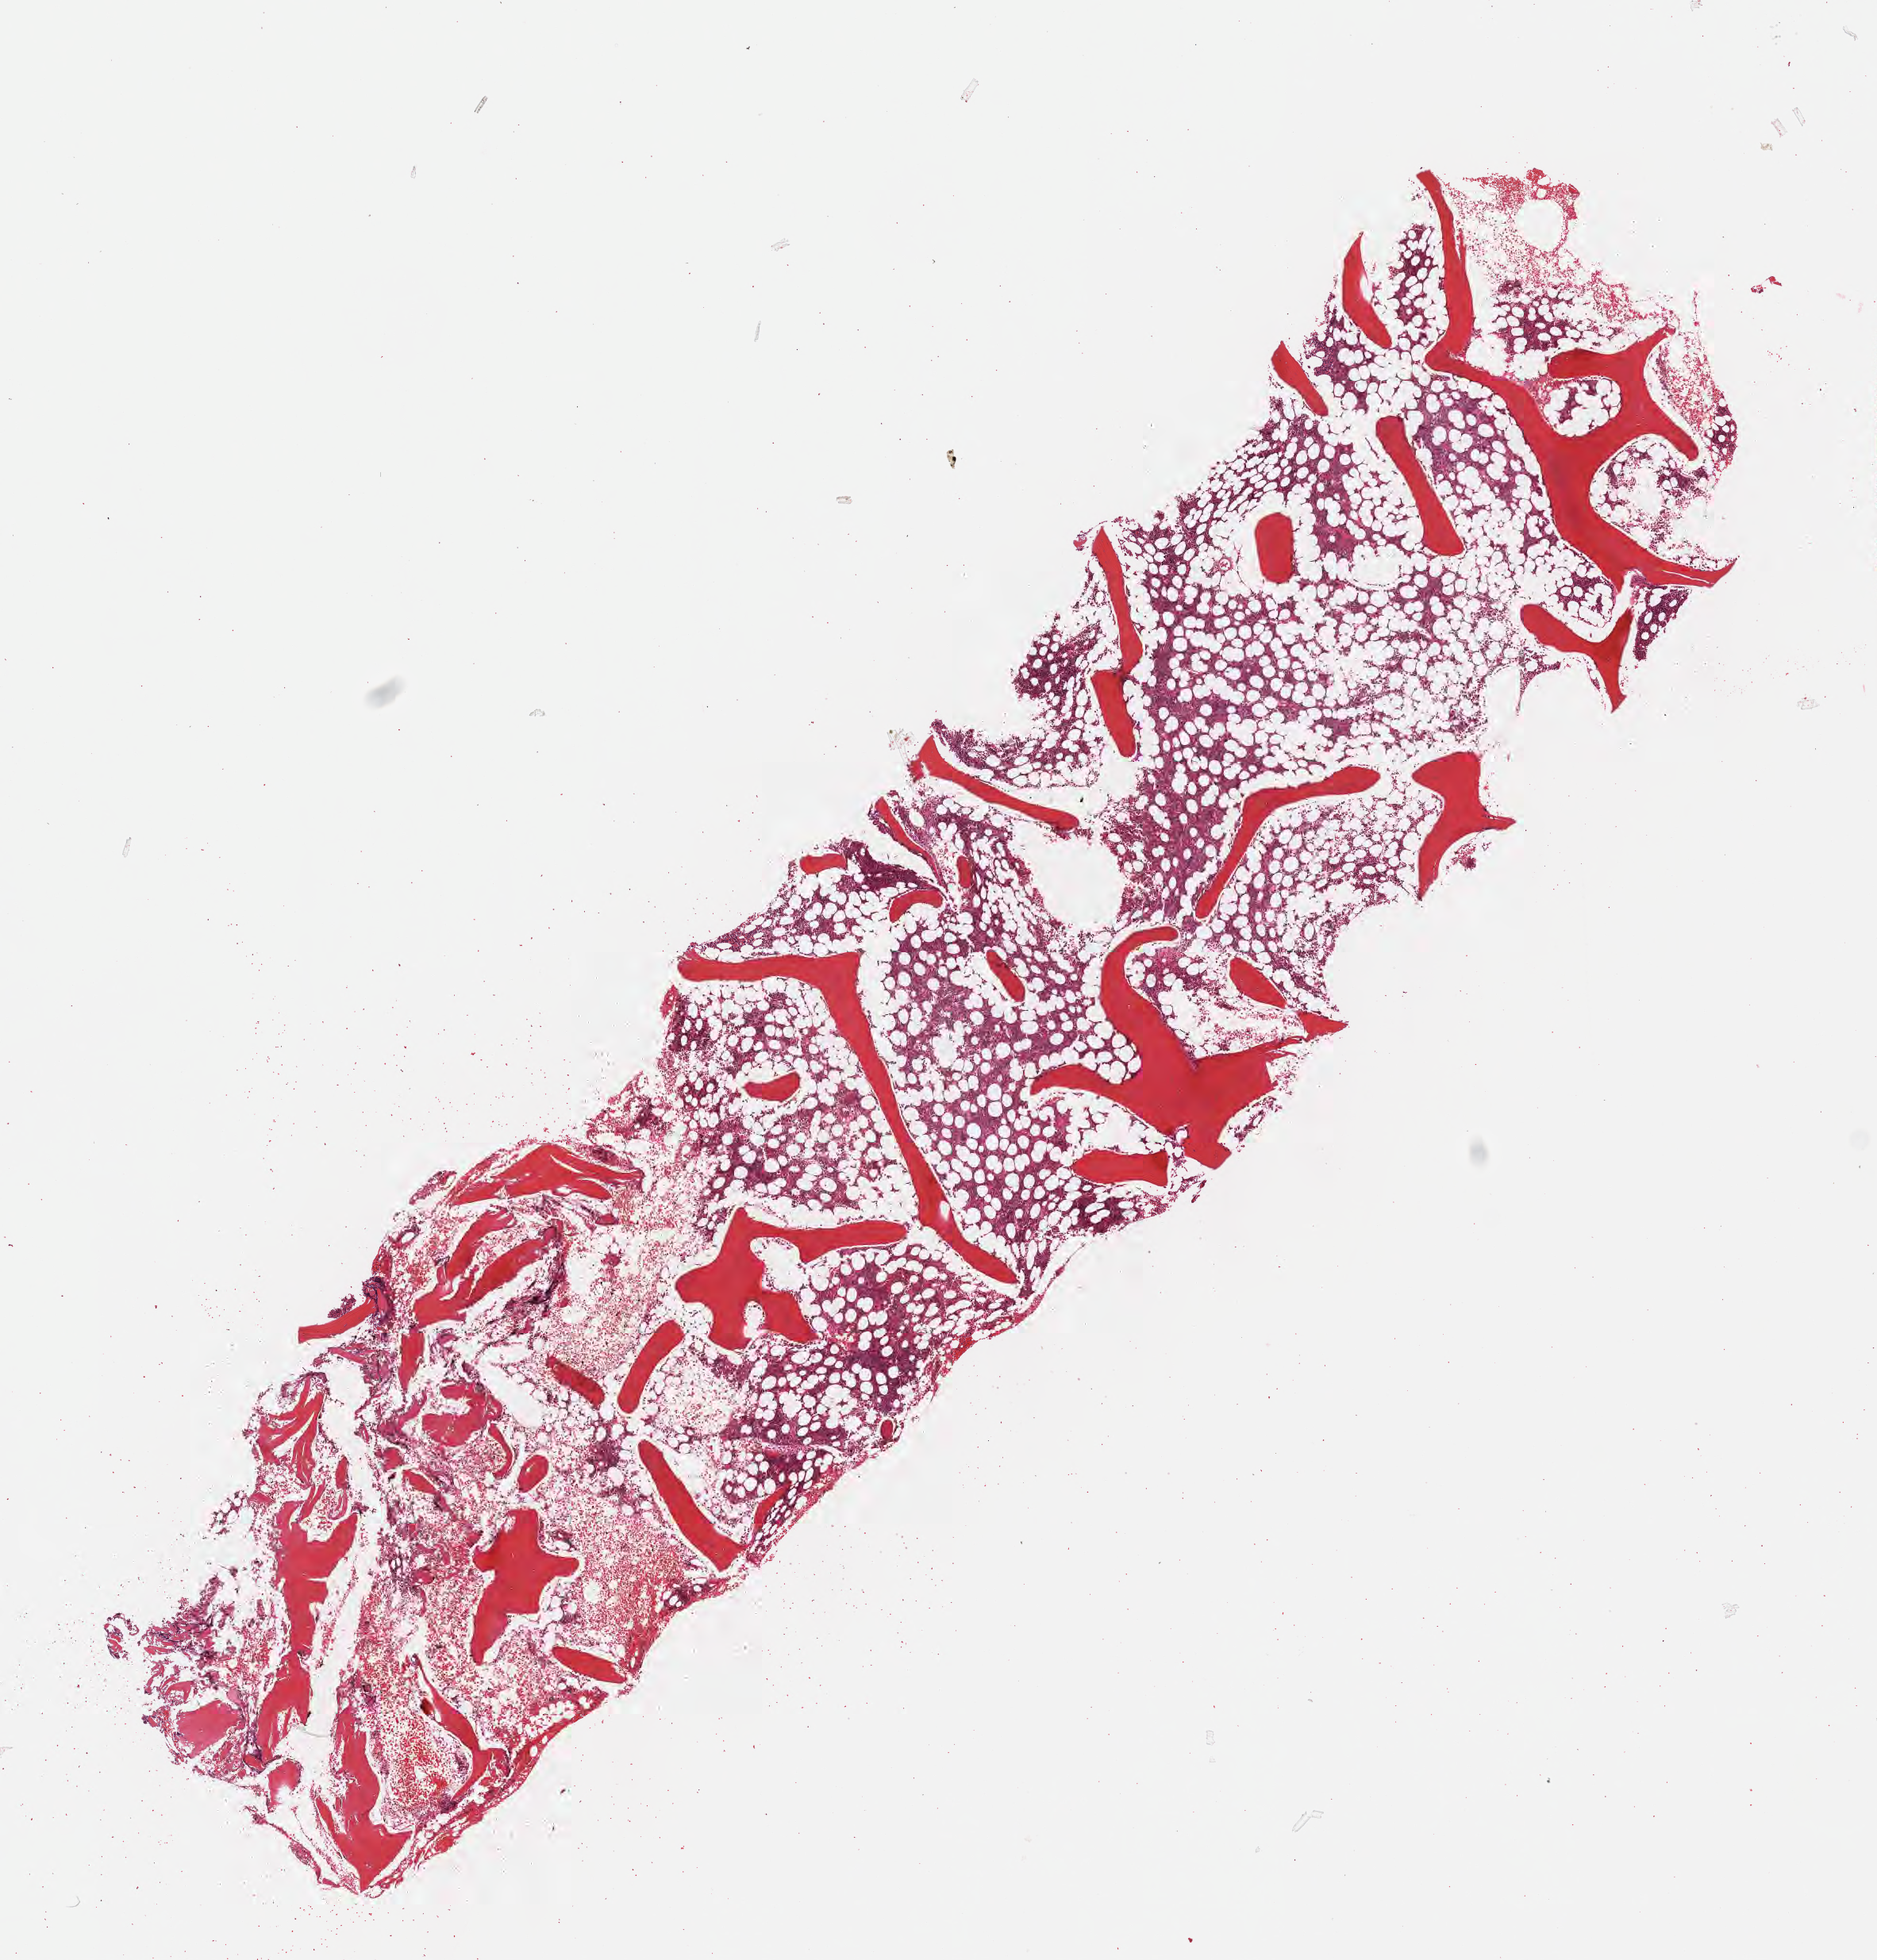
Whole-slide image, hematoxylin and eosin (H&E) stain, a low-resolution overview of the entire scanned area, about 9.6 x 10.0 mm, formalin-fixed paraffin-embedded section, specimen: non-tumor (normal tissue) sample from a patient with burkitt lymphoma, NOS. Male patient, 40 years old. Pathologist review of this section (percent, as recorded): tumor cells 0%, tumor nuclei 0%, stromal cells 0%, necrosis 0%, normal cells 100%. Infiltration values recorded for this section: lymphocyte infiltration 20%, monocyte infiltration 10%, neutrophil infiltration 50%.
This section: non-tumor tissue sample; the patient's diagnosis is given above. Section: top of the tissue portion.